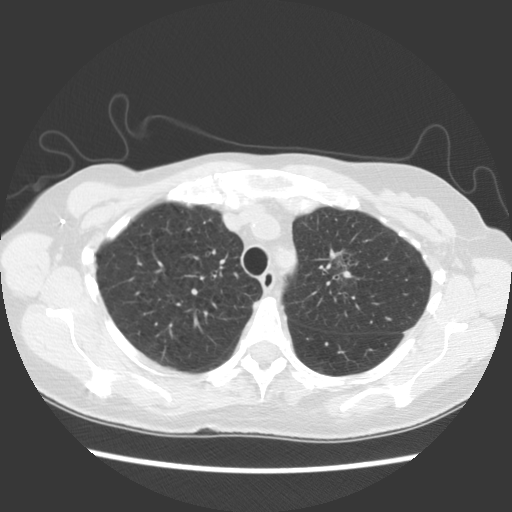
Low-dose screening chest CT, axial slice, baseline annual screen, lung window (W 1500 / L -600 HU), 2.5 mm slice thickness, slice 96 of 129 in the series, 512 × 512 image matrix, field of view 325 × 325 mm. Female participant, aged 65 years at enrolment.
Expert-annotated lung lesion, bounding box <313,234,380,296> (left, top, right, bottom; pixels). The exam's reader record, not a measurement of the box and not confirmed to be the same lesion: non-calcified nodule or mass ≥4 mm, left upper lobe, 11 × 10 mm, poorly defined margins, ground glass attenuation. Official screen result: positive, change unspecified: nodule(s) >= 4 mm or enlarging nodule(s), mass(es), or other non-specific abnormalities suspicious for lung cancer. Lung cancer was diagnosed 810 days after this screen (after the third annual screen): adenocarcinoma, NOS, left upper lobe, moderately differentiated (G2), stage IA (AJCC 6th edition), 30 mm at pathology.